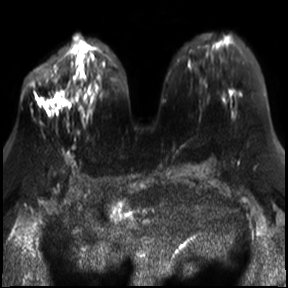
Breast MRI, one axial slice; slice 15 of 30 in the series (ordered by position); diffusion-weighted series; image 2 of 4 stored at this slice position (different b-values; order by instance number); 3 T; 4 mm slice thickness; 288 × 288 image matrix, field of view 340 × 340 mm. Female patient.
Annotated regions visible in this slice (expert manual segmentation):
- tumour on diffusion-weighted imaging: box from (x=44, y=100) to (x=60, y=116) px